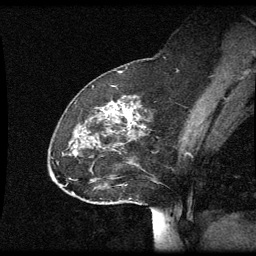
Breast MRI (dynamic contrast-enhanced), one sagittal slice. Position 22 of 60 along the scan axis. Dynamic contrast-enhanced series, image 2 of 3 at this slice position (ordered by acquisition). 1.5 T. TE 4.2 ms, TR 8.9 ms. 2 mm slice thickness. 256 × 256 image matrix. Female patient, age 49 years. From the clinical record (not read from this slice): setting: breast cancer imaged before/during neoadjuvant chemotherapy; receptor status: HR-positive, HER2-negative.
Structures marked on this image (semi-automatically segmented with operator editing):
- analysis volume of interest (the breast-tissue region the enhancement analysis was run in; not a lesion): bounding box [x1, y1, x2, y2] px = [50, 94, 159, 205]
- tumour enhancement mask (voxels above the 70 % enhancement threshold inside the analysis volume of interest): [106, 108, 137, 127]